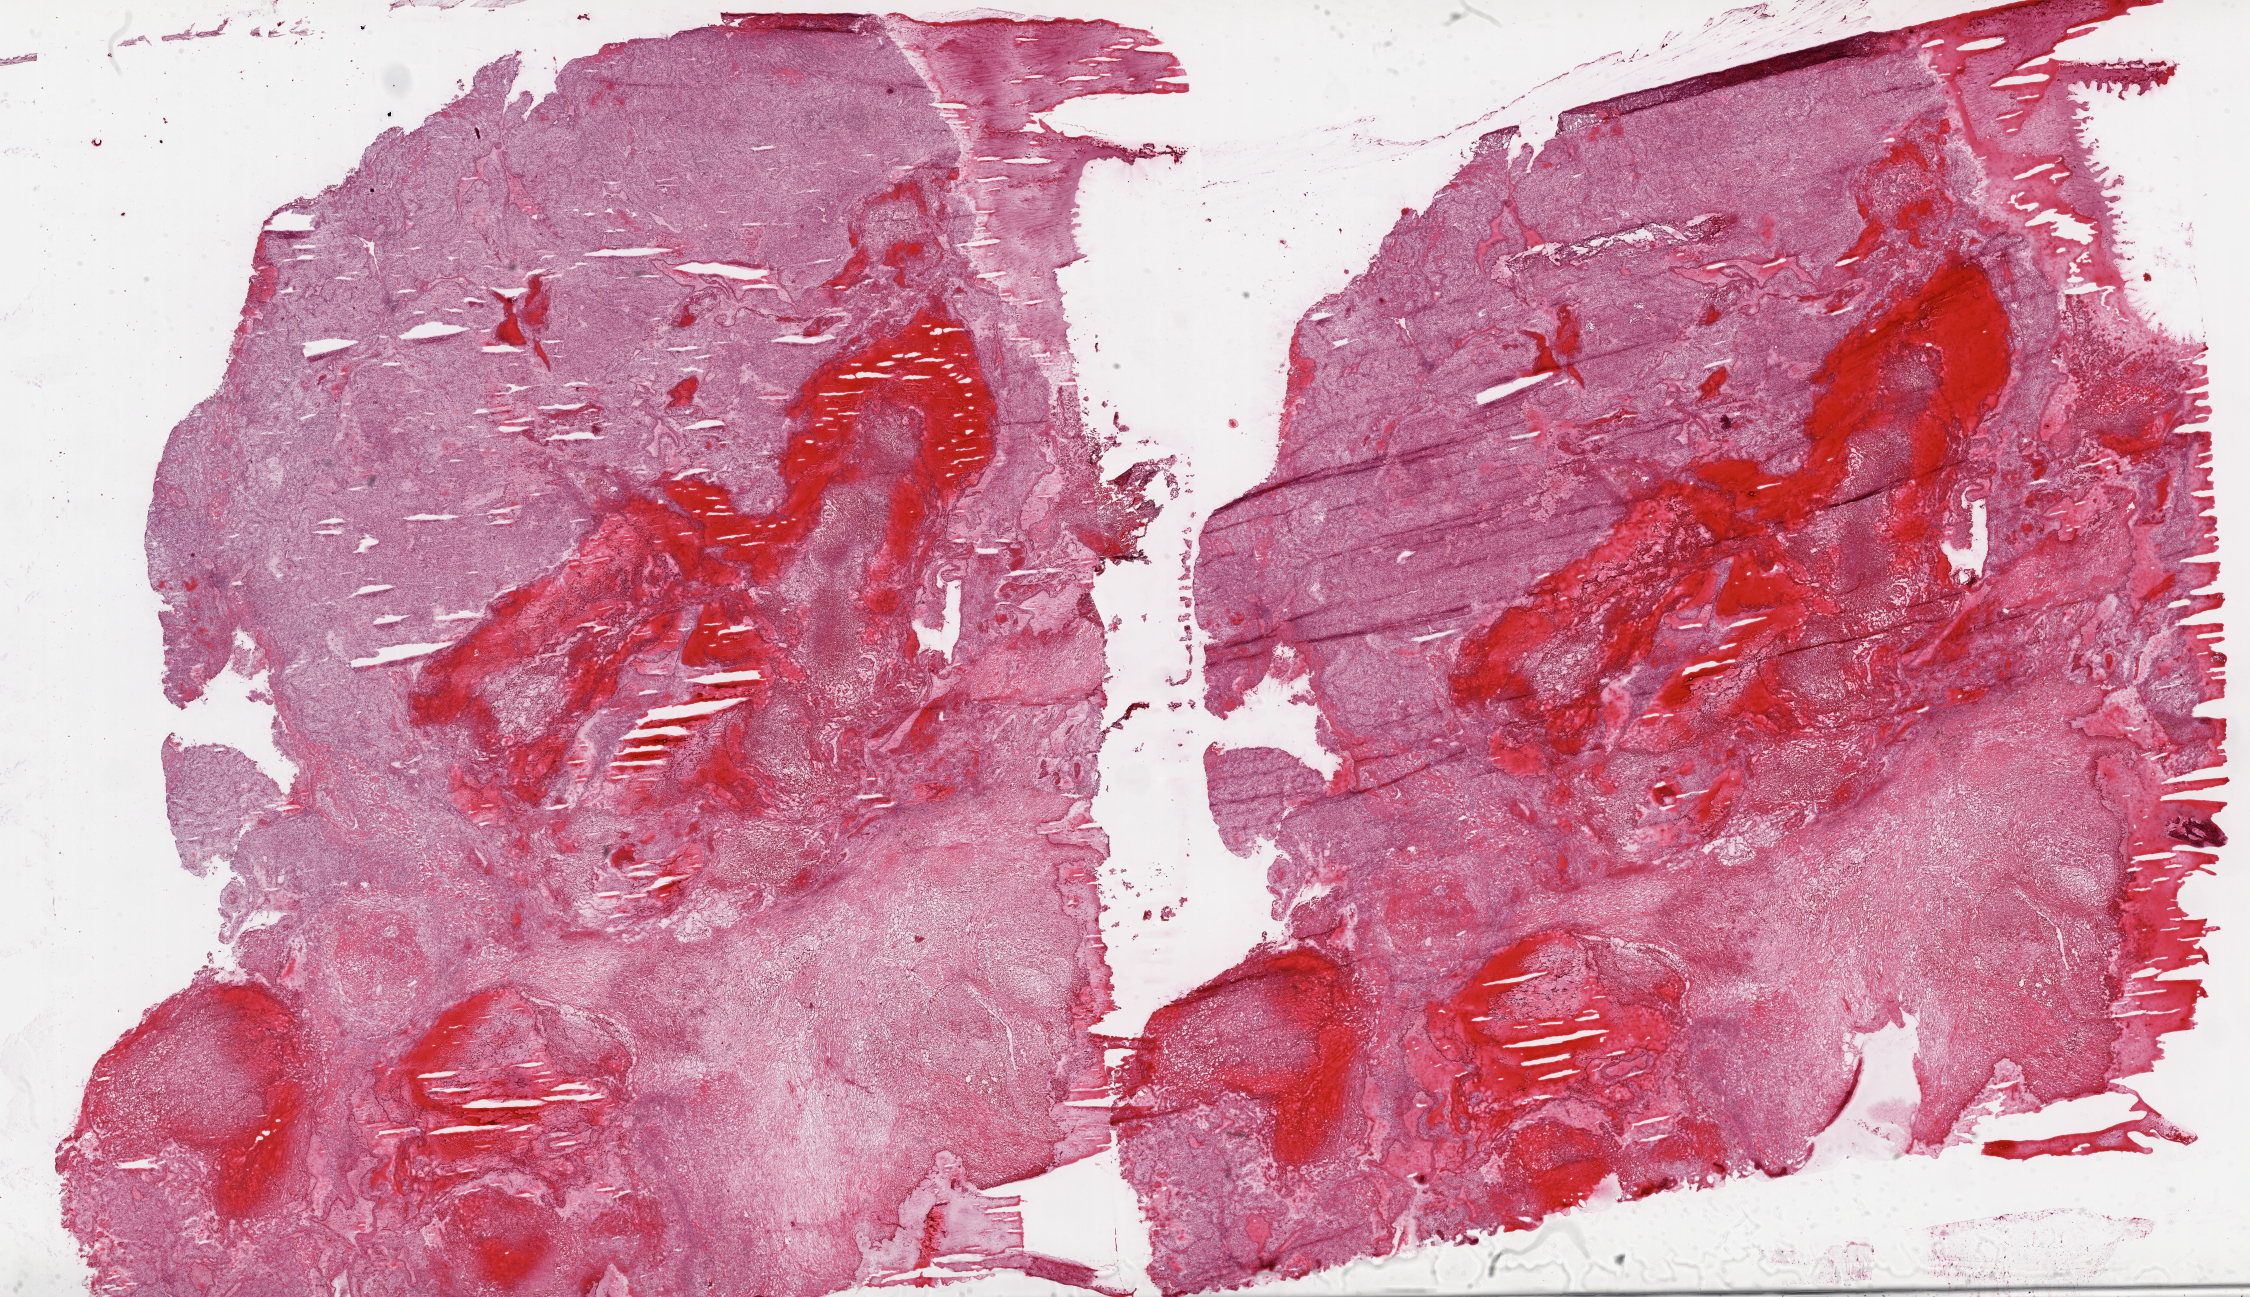
Digitized H&E-stained tissue section (whole slide) — low-resolution overview of the scanned area, about 36.1 x 20.8 mm; frozen section from the top of the tissue portion; primary tumour sample from the kidney. Male patient; age at initial diagnosis 72 years. Histologic grade: G3 (poorly differentiated). Slide review estimates, as recorded: tumour cells 75%, tumour nuclei 80%, normal cells 0%, stromal cells 25%, necrosis 0%.
* diagnosis: Clear cell adenocarcinoma, NOS
* lymph nodes positive (case pathology): 0 of 9 examined
* AJCC pathologic stage: III